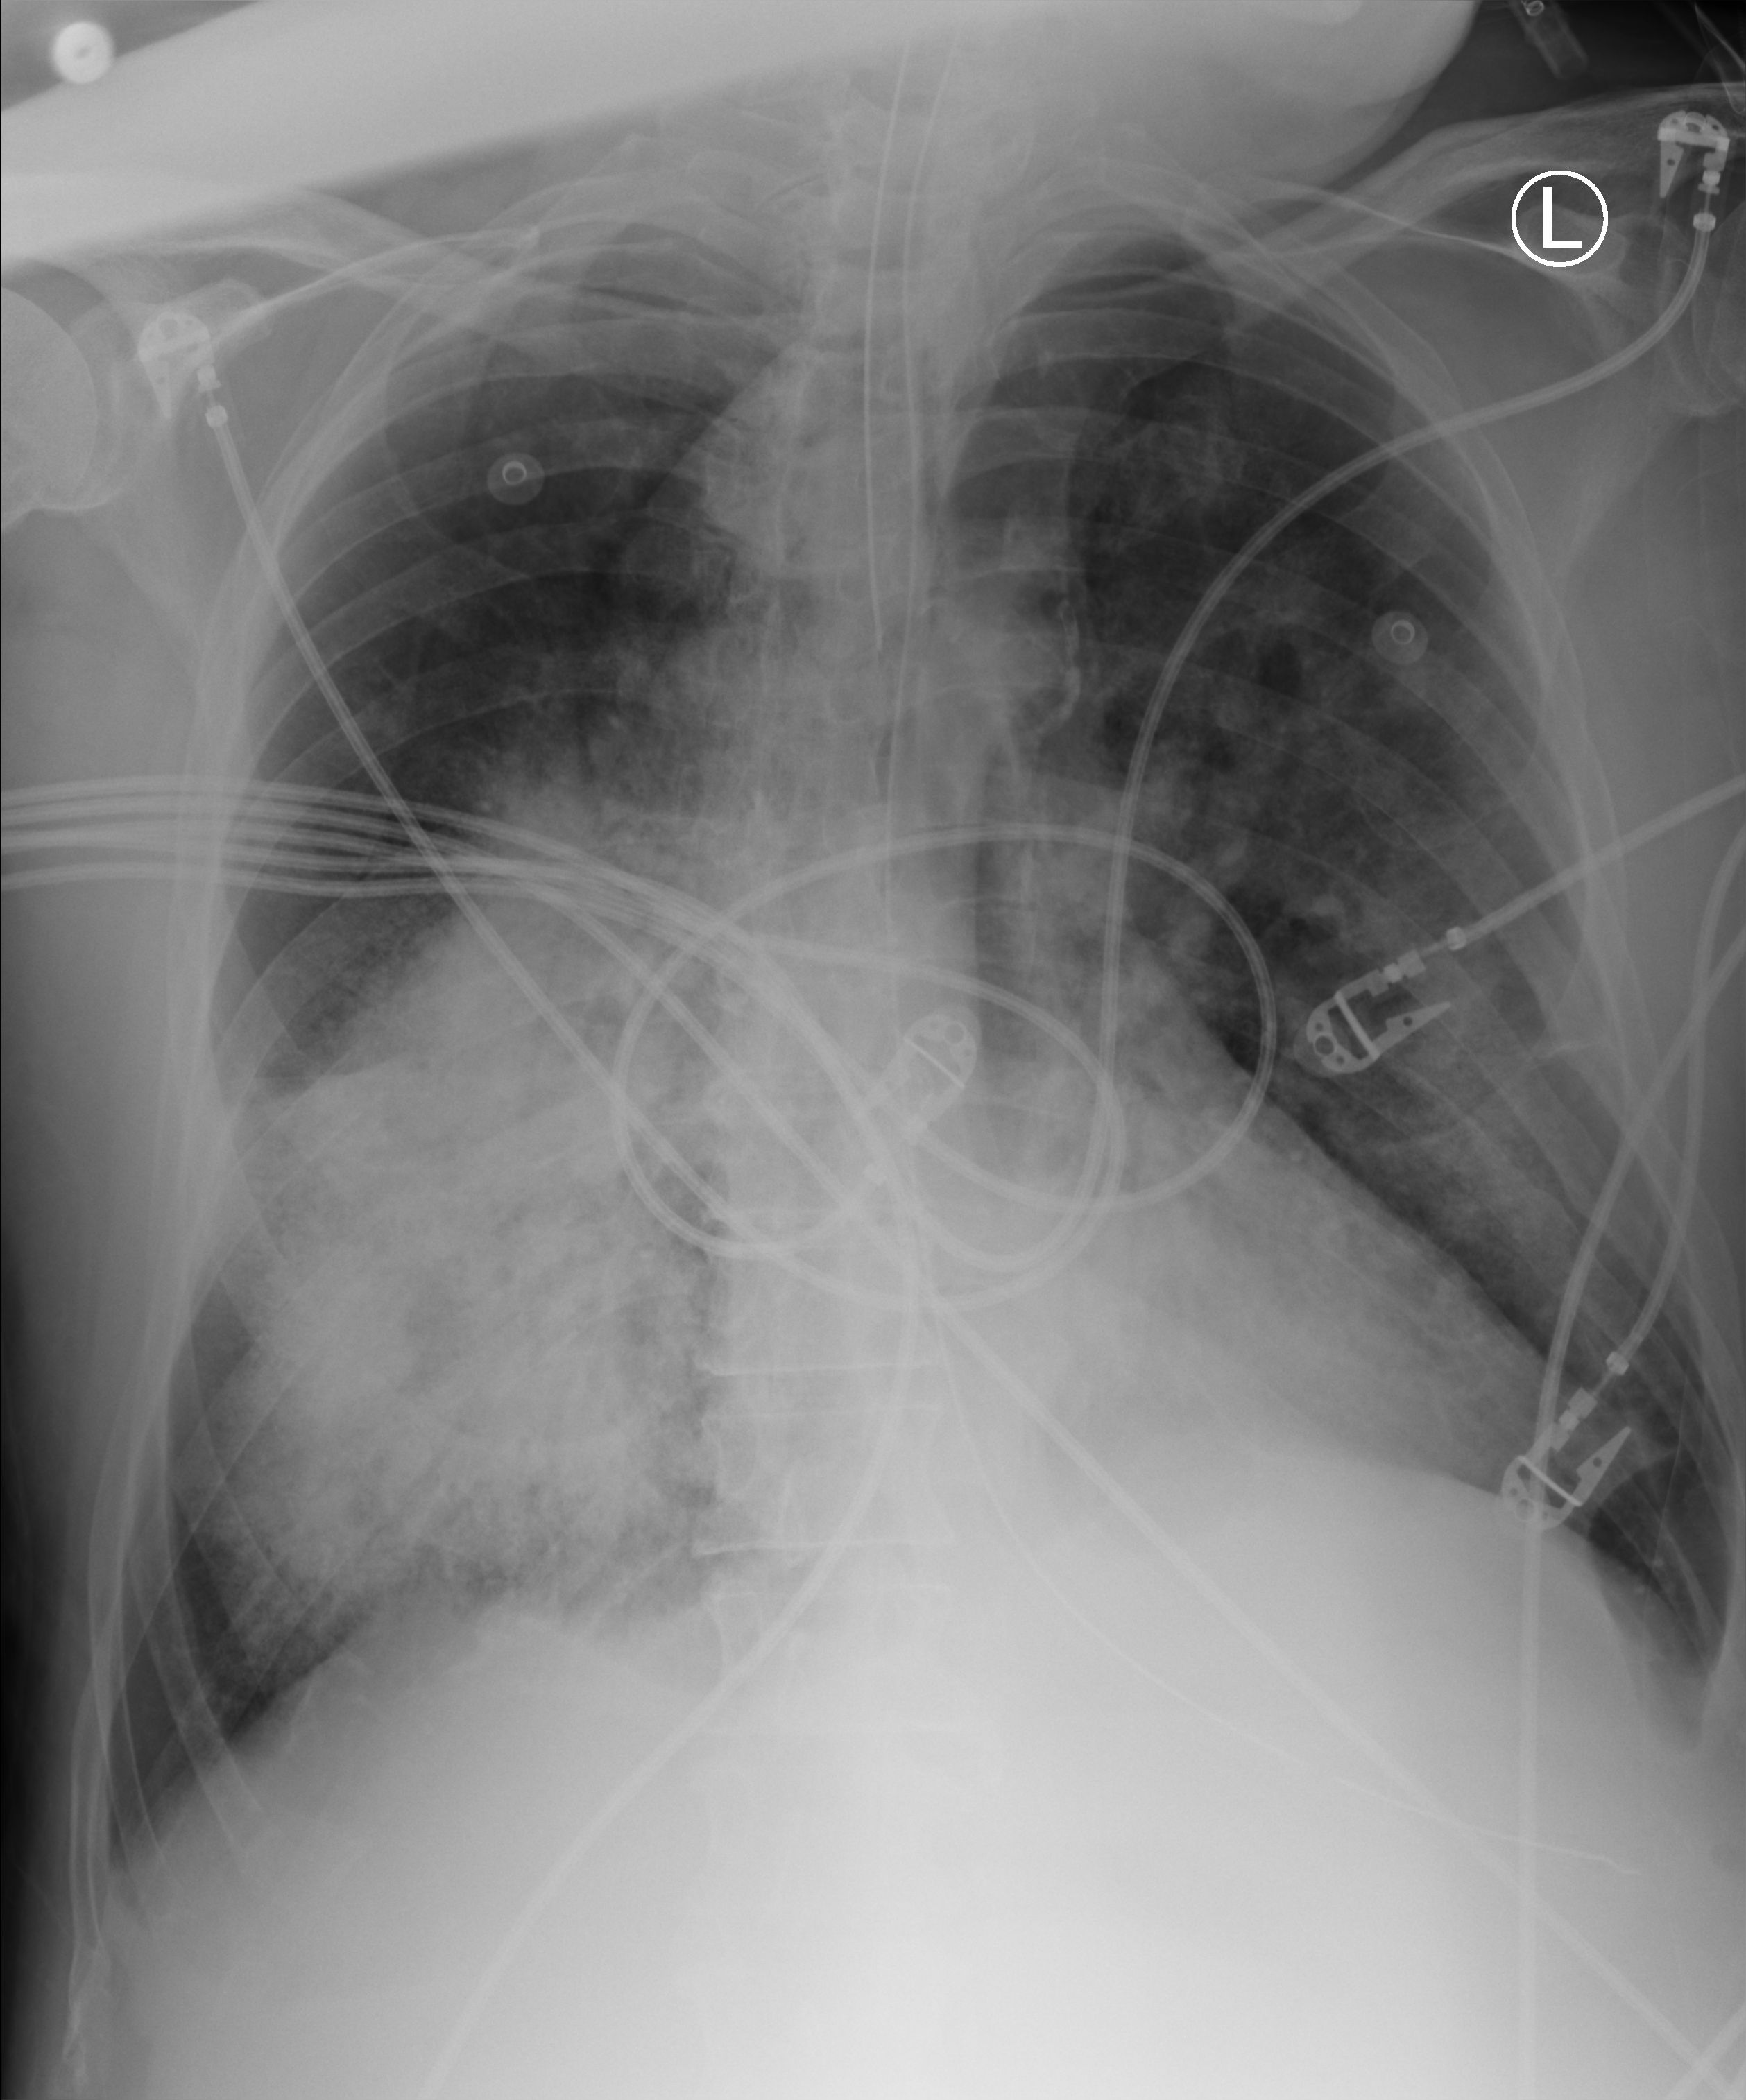
Bedside chest radiograph (computed radiography); anteroposterior (AP) projection. Patient hospitalised with COVID-19; male, aged 60–74 years.
Admission-level facts for this patient (not findings on this image; timing relative to this image not recorded): mechanically ventilated during this hospital stay: yes.